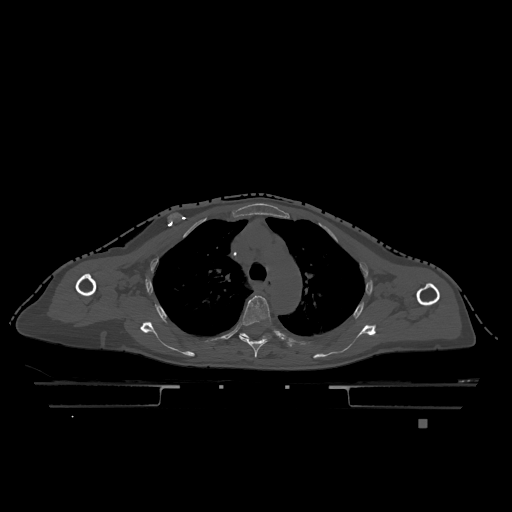
CT including the spine, one axial slice; slice 871 of 1317 in the series (ordered by position); bone window (W 1800 / L 400 HU); 0.5 mm slice thickness; 512 × 512 image matrix, field of view 500 × 500 mm. Patient: female, 74 years. Case-level facts recorded for this patient, not image findings: primary cancer: lung; vertebrae with lytic lesions (as recorded): T1, T4, T5, T6, L4, L5.
Structures marked on this image (semi-automatic segmentation, software-assisted and operator-edited):
- T4 vertebra: box from (x=239, y=296) to (x=271, y=358) px
- T5 vertebra: (x=240, y=333)–(x=266, y=338)